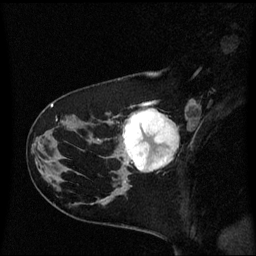
Breast MRI (dynamic contrast-enhanced), one sagittal slice; position 20 of 60 along the scan axis; dynamic contrast-enhanced series, image 2 of 3 at this slice position (ordered by acquisition); 1.5 T; TE 4.2 ms, TR 8.4 ms; 2 mm slice thickness; 256 × 256 image matrix, field of view 220 × 220 mm. Female patient, age 41 years. Case-level facts recorded for this patient, not image findings: setting: breast cancer imaged before/during neoadjuvant chemotherapy; receptor status: triple-negative.
Outlined on this slice (semi-automatic segmentation, software-assisted and operator-edited):
- analysis volume of interest (the breast-tissue region the enhancement analysis was run in; not a lesion): box from (x=116, y=106) to (x=178, y=177) px
- tumour enhancement mask (voxels above the 70 % enhancement threshold inside the analysis volume of interest): (x=123, y=108)–(x=178, y=173)